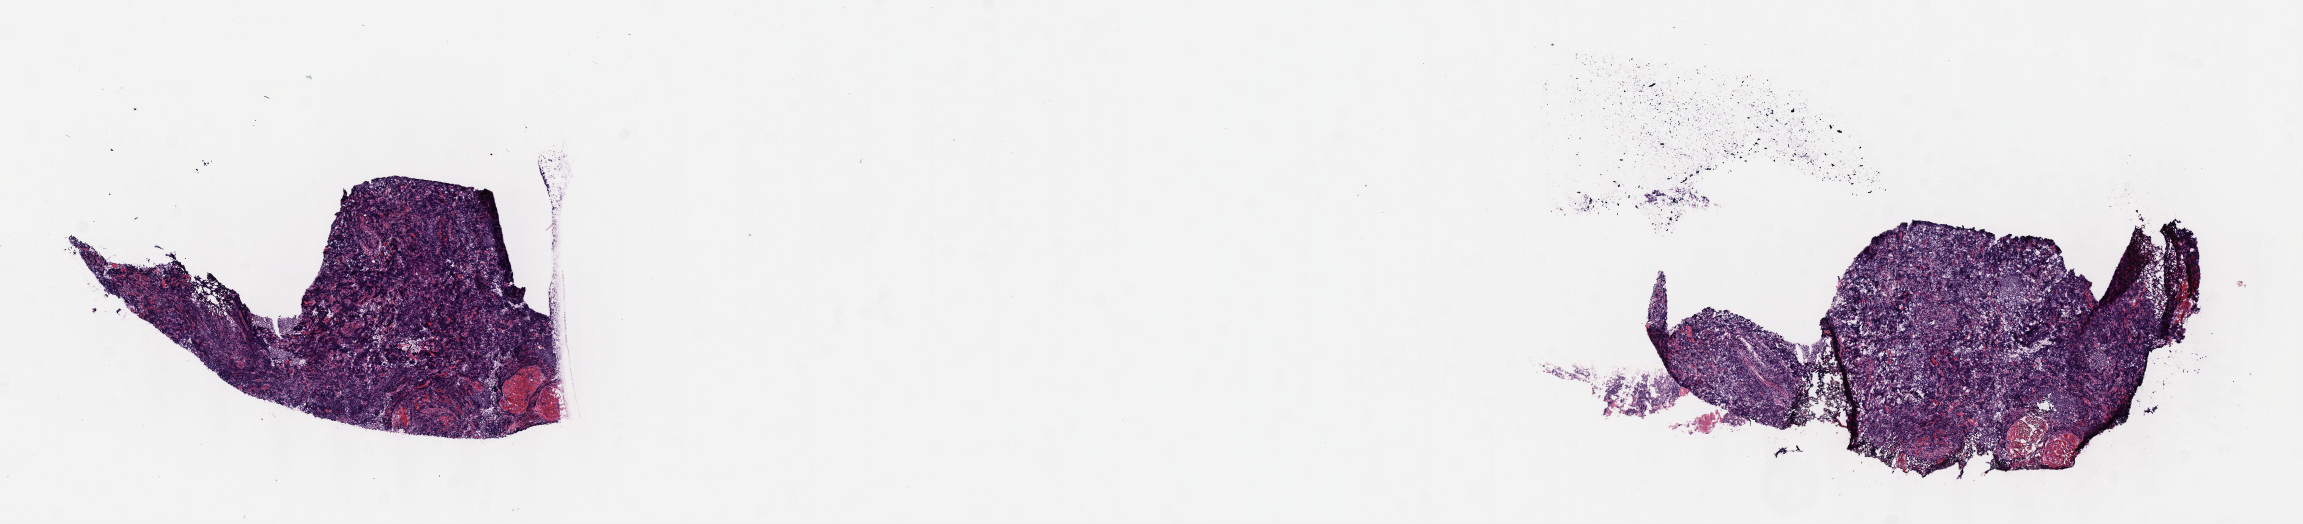
Whole-slide image, haematoxylin and eosin stain, low-resolution overview of the scanned area, about 18.6 x 4.2 mm. Cryosection. Specimen: primary tumor. Site: cranium. Male patient, aged 11. Slide review estimates, as recorded: tumor cells 80%, tumor nuclei 90%, stromal cells 20%, necrosis 0%, normal cells 0%. Inflammatory infiltration, as recorded: lymphocyte infiltration 10%, monocyte infiltration 10%, neutrophil infiltration 0%.
Section: top of the tissue portion. Ann Arbor stage (patient): Stage I. Histologic diagnosis: Burkitt lymphoma, NOS.